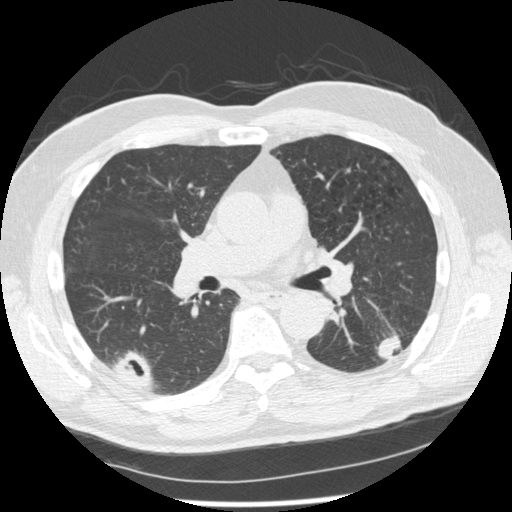
Chest CT (low-dose screening protocol), one axial image, second annual screen, lung window (W 1500 / L -600 HU), standard (soft-tissue) reconstruction kernel (STANDARD), 120 kVp. Male participant, aged 74 years at enrolment. Former smoker at enrolment.
• Expert-annotated lung lesion, bounding box [x1, y1, x2, y2] px = [371, 316, 421, 369].
• The screening reader recorded 7 non-calcified nodules or masses ≥4 mm on this exam (right upper lobe, right lower lobe, right upper lobe, right lower lobe, left lower lobe, left upper lobe, left upper lobe); which of them this box marks is not recorded.
• Lung cancer was diagnosed 43 days after this screen: squamous cell carcinoma, NOS, left lower lobe, well differentiated (G1), stage IA (AJCC 6th edition), 28 mm at pathology.